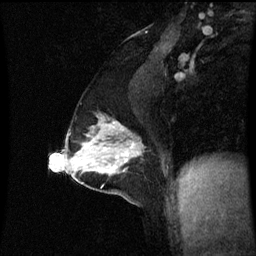
Breast MRI (dynamic contrast-enhanced), one sagittal slice; position 37 of 60 along the scan axis; dynamic contrast-enhanced series, image 2 of 3 at this slice position (ordered by acquisition); 1.5 T; TE 4.2 ms, TR 8.9 ms; 2.1 mm slice thickness; 256 × 256 image matrix, field of view 200 × 200 mm. Patient: female, 47 years. Case-level facts recorded for this patient, not image findings: setting: breast cancer imaged before/during neoadjuvant chemotherapy; receptor status: HR-positive, HER2-negative.
Structures marked on this image (semi-automatic segmentation, software-assisted and operator-edited):
- analysis volume of interest (the breast-tissue region the enhancement analysis was run in; not a lesion): bounding box (x1, y1, x2, y2) in pixels: (71, 116, 144, 163)
- tumour enhancement mask (voxels above the 70 % enhancement threshold inside the analysis volume of interest): (95, 122, 140, 155)